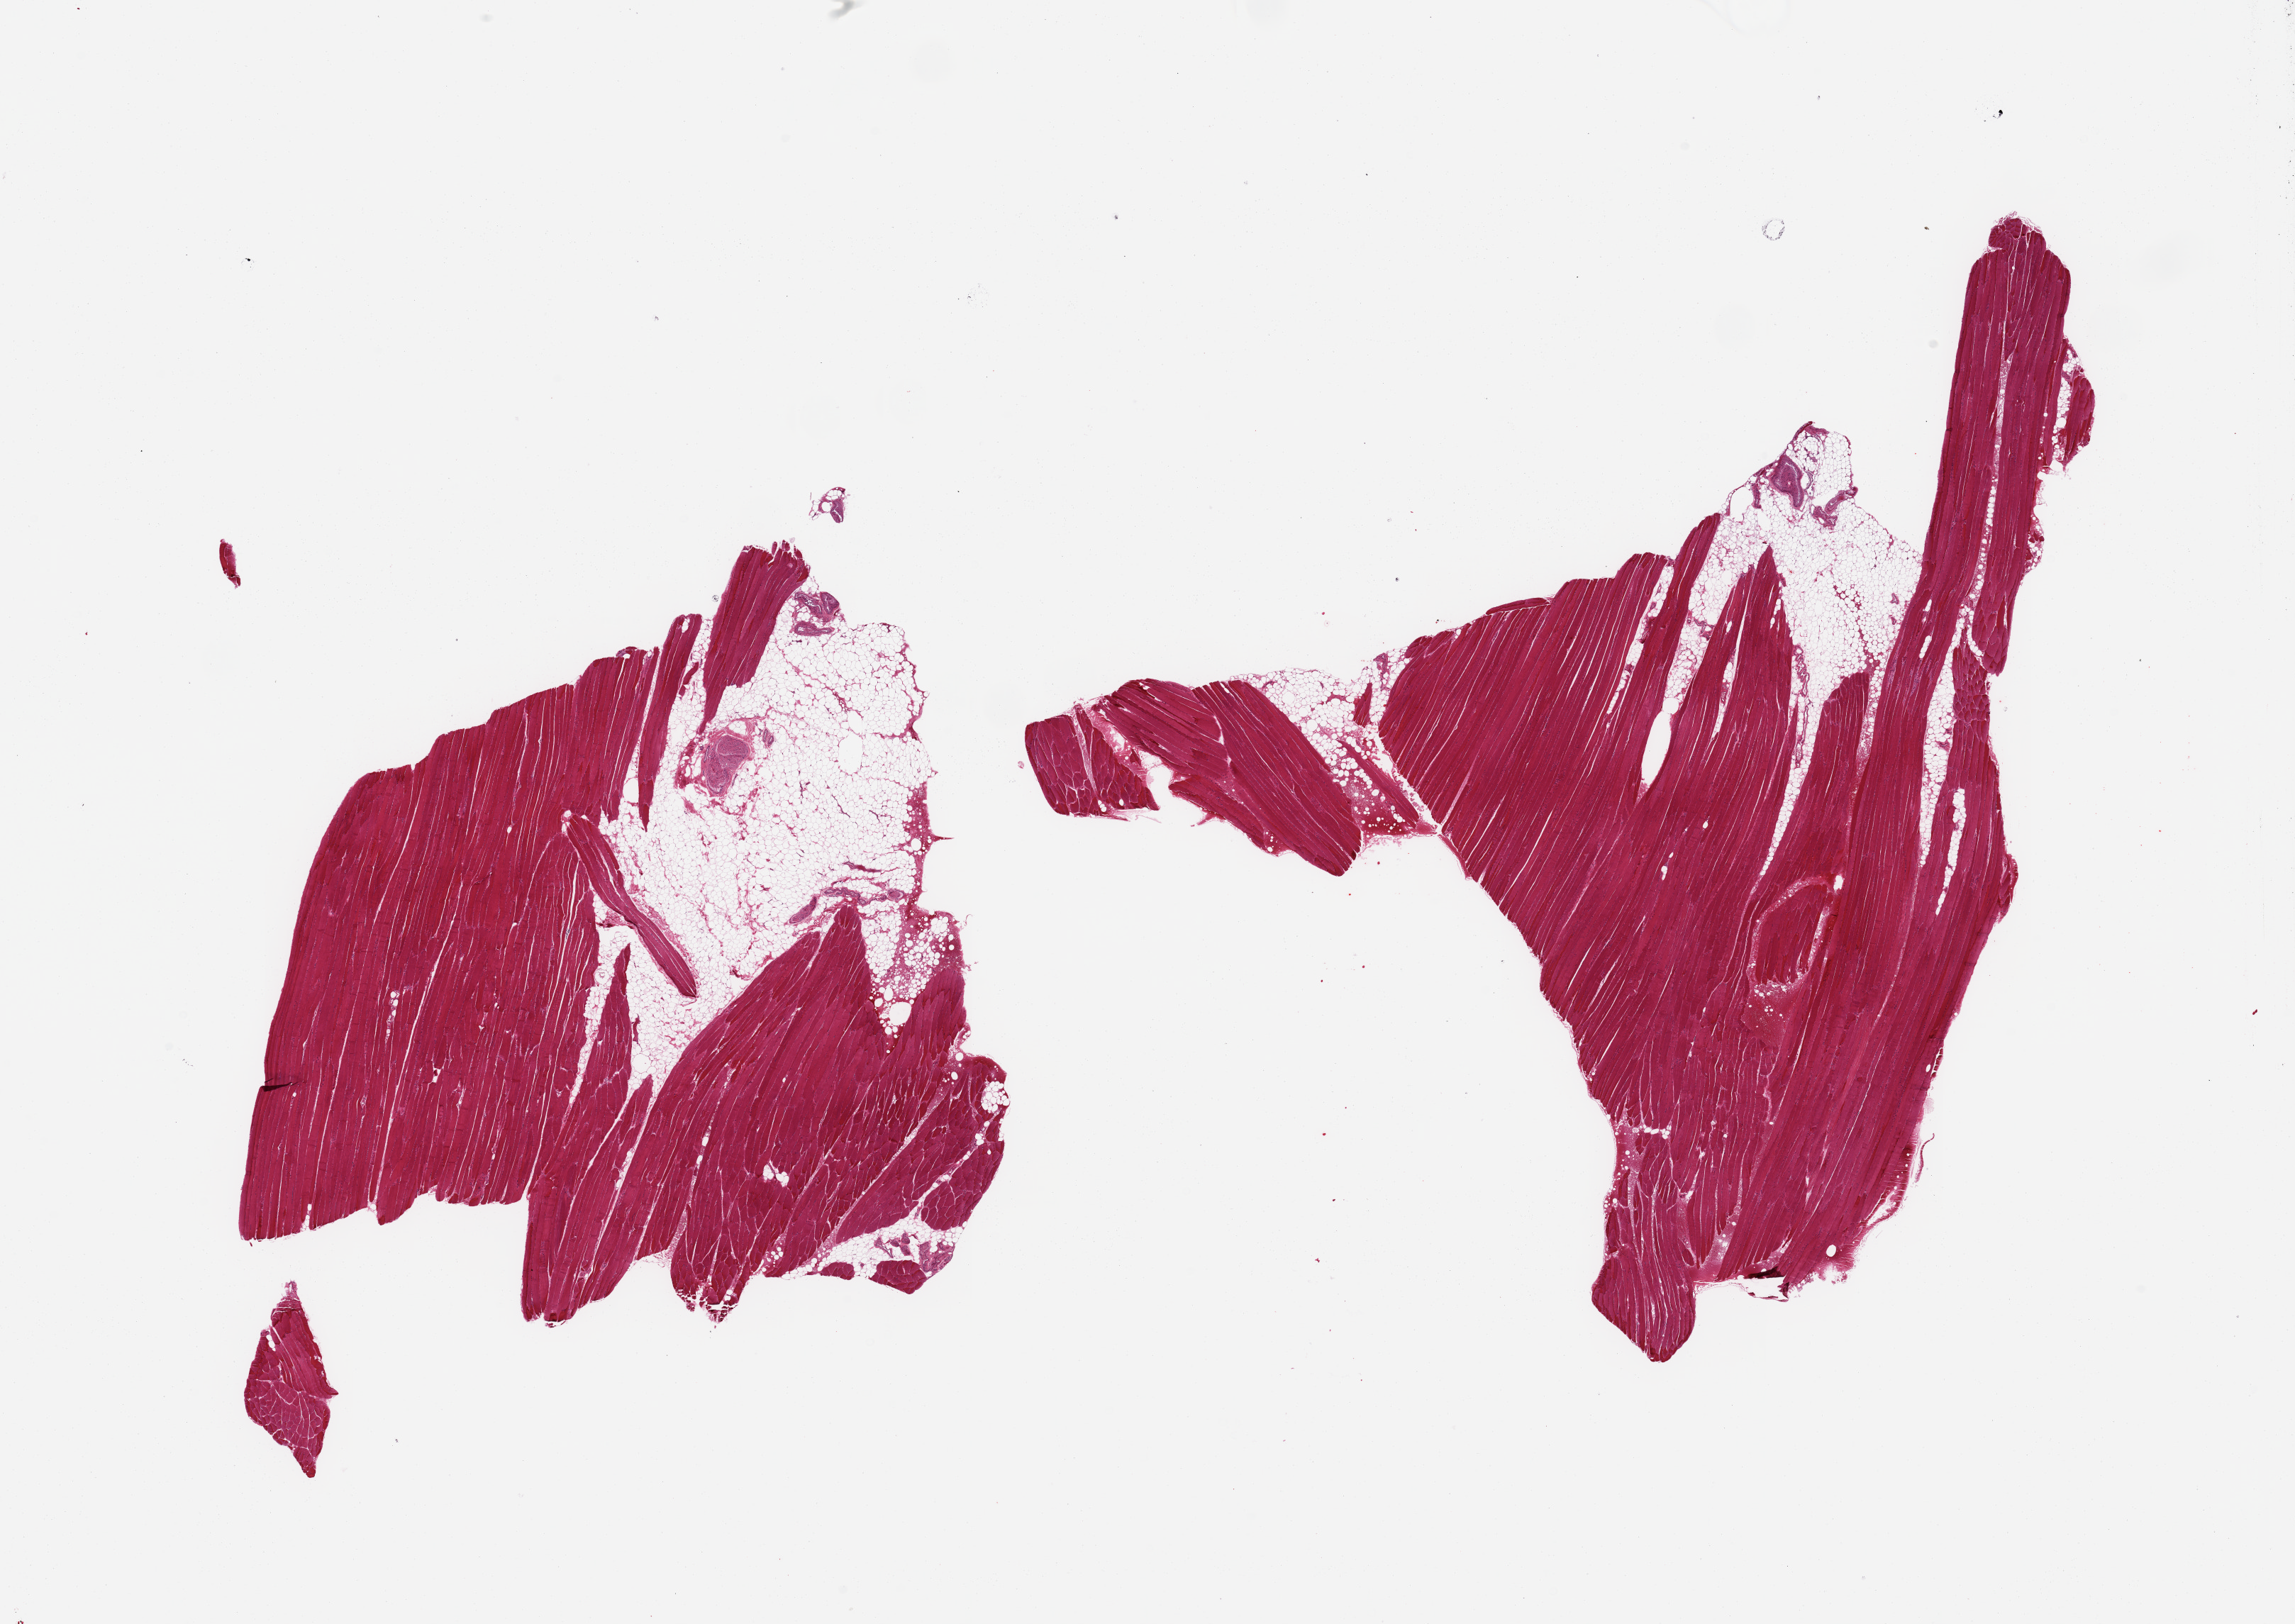
Digitized hematoxylin and eosin (H&E)-stained section — whole scanned area (about 25.6 x 18.1 mm) shown as a low-resolution overview, PAXgene-fixed, paraffin-embedded tissue, section of skeletal muscle (target tissue), donor tissue sample. Donor: male.
Pathologist's review note for this sample: 2 pieces, ~25% interstitial/adherent fat/vascular elements.